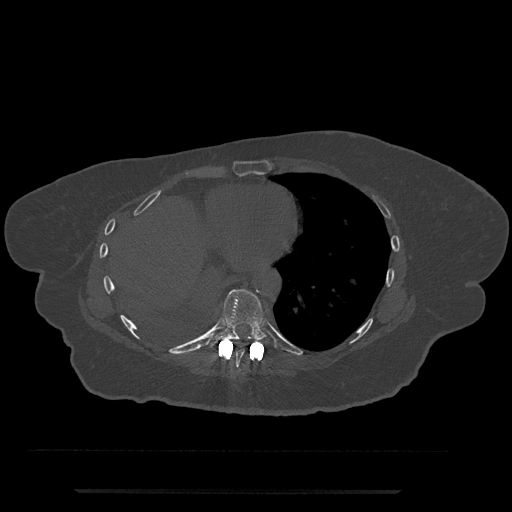
CT including the spine, one axial slice; slice 356 of 797 in the series (ordered by position); bone window (W 1800 / L 400 HU); 0.5 mm slice thickness; 512 × 512 image matrix, field of view 440 × 440 mm. Patient: female, 51 years. Case-level facts recorded for this patient, not image findings: primary cancer: neuro.
Outlined on this slice (semi-automatically segmented with operator editing):
- T8 vertebra: bounding box (x1, y1, x2, y2) in pixels: (230, 347, 246, 373)
- T9 vertebra: (209, 289, 274, 348)